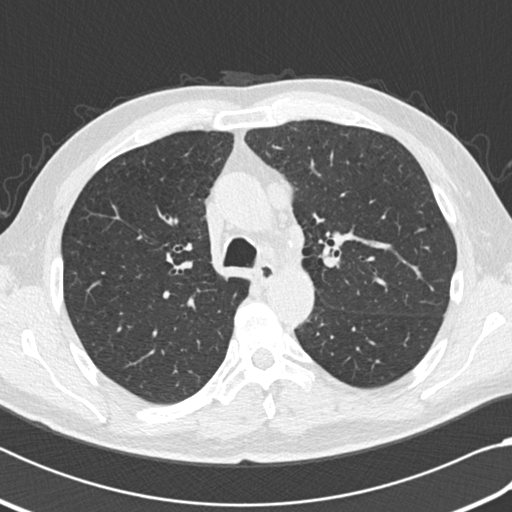
Axial slice from a low-dose chest CT screening exam, third annual screen, lung window (W 1500 / L -600 HU), 2 mm slice thickness, standard (soft-tissue) reconstruction kernel (B30f). Male, age 64 years at enrolment. Current smoker at enrolment.
- Lesion marked by an expert reader, box from (x=252, y=177) to (x=289, y=214) px.
- Screening reader's record for this exam: no non-calcified nodule ≥4 mm recorded.
- Official screen result: negative screen, significant abnormalities not suspicious for lung cancer.
- Lung cancer was diagnosed 163 days after this screen: small cell carcinoma, NOS, mediastinum, stage IV (AJCC 6th edition).